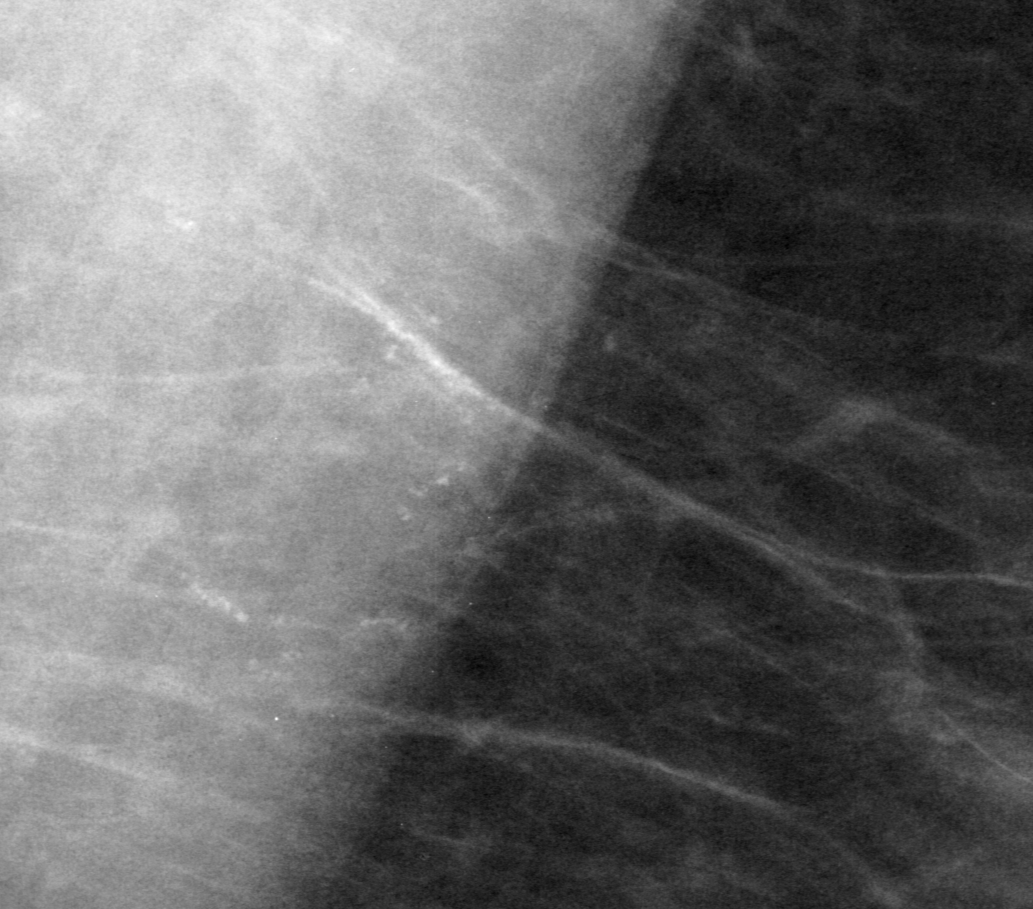
Region of interest cut from a scanned film mammogram (one marked finding), left breast, MLO view, BI-RADS breast density category 2 (scale 1–4).
- Finding: calcifications, morphology amorphous, distribution linear; BI-RADS assessment category 3; pathology result (as recorded, not read from the image): malignant.